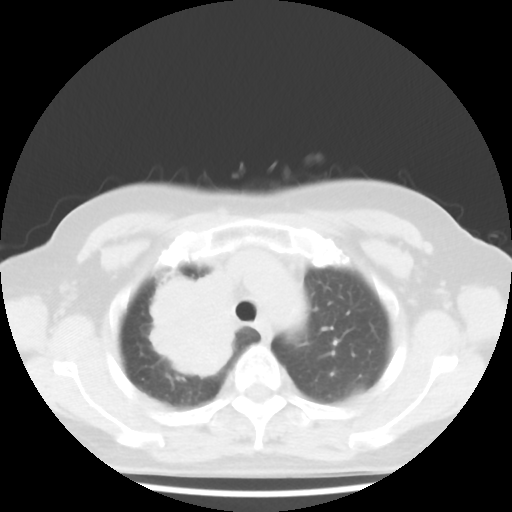
Chest CT, one axial slice. Slice 34 of 43 in the series (ordered by position). 100 kVp. Lung window (W 1500 / L -600 HU). 512 × 512 image matrix, field of view 316 × 316 mm. Female patient, age 62 years. Case-level facts recorded for this patient, not image findings: clinical TNM (as recorded): T3 N0 M0.
Outlined on this slice (bounding box drawn by a radiologist):
- lung tumour (recorded histology: small cell carcinoma): bounding box <145,271,236,384> (left, top, right, bottom; pixels)